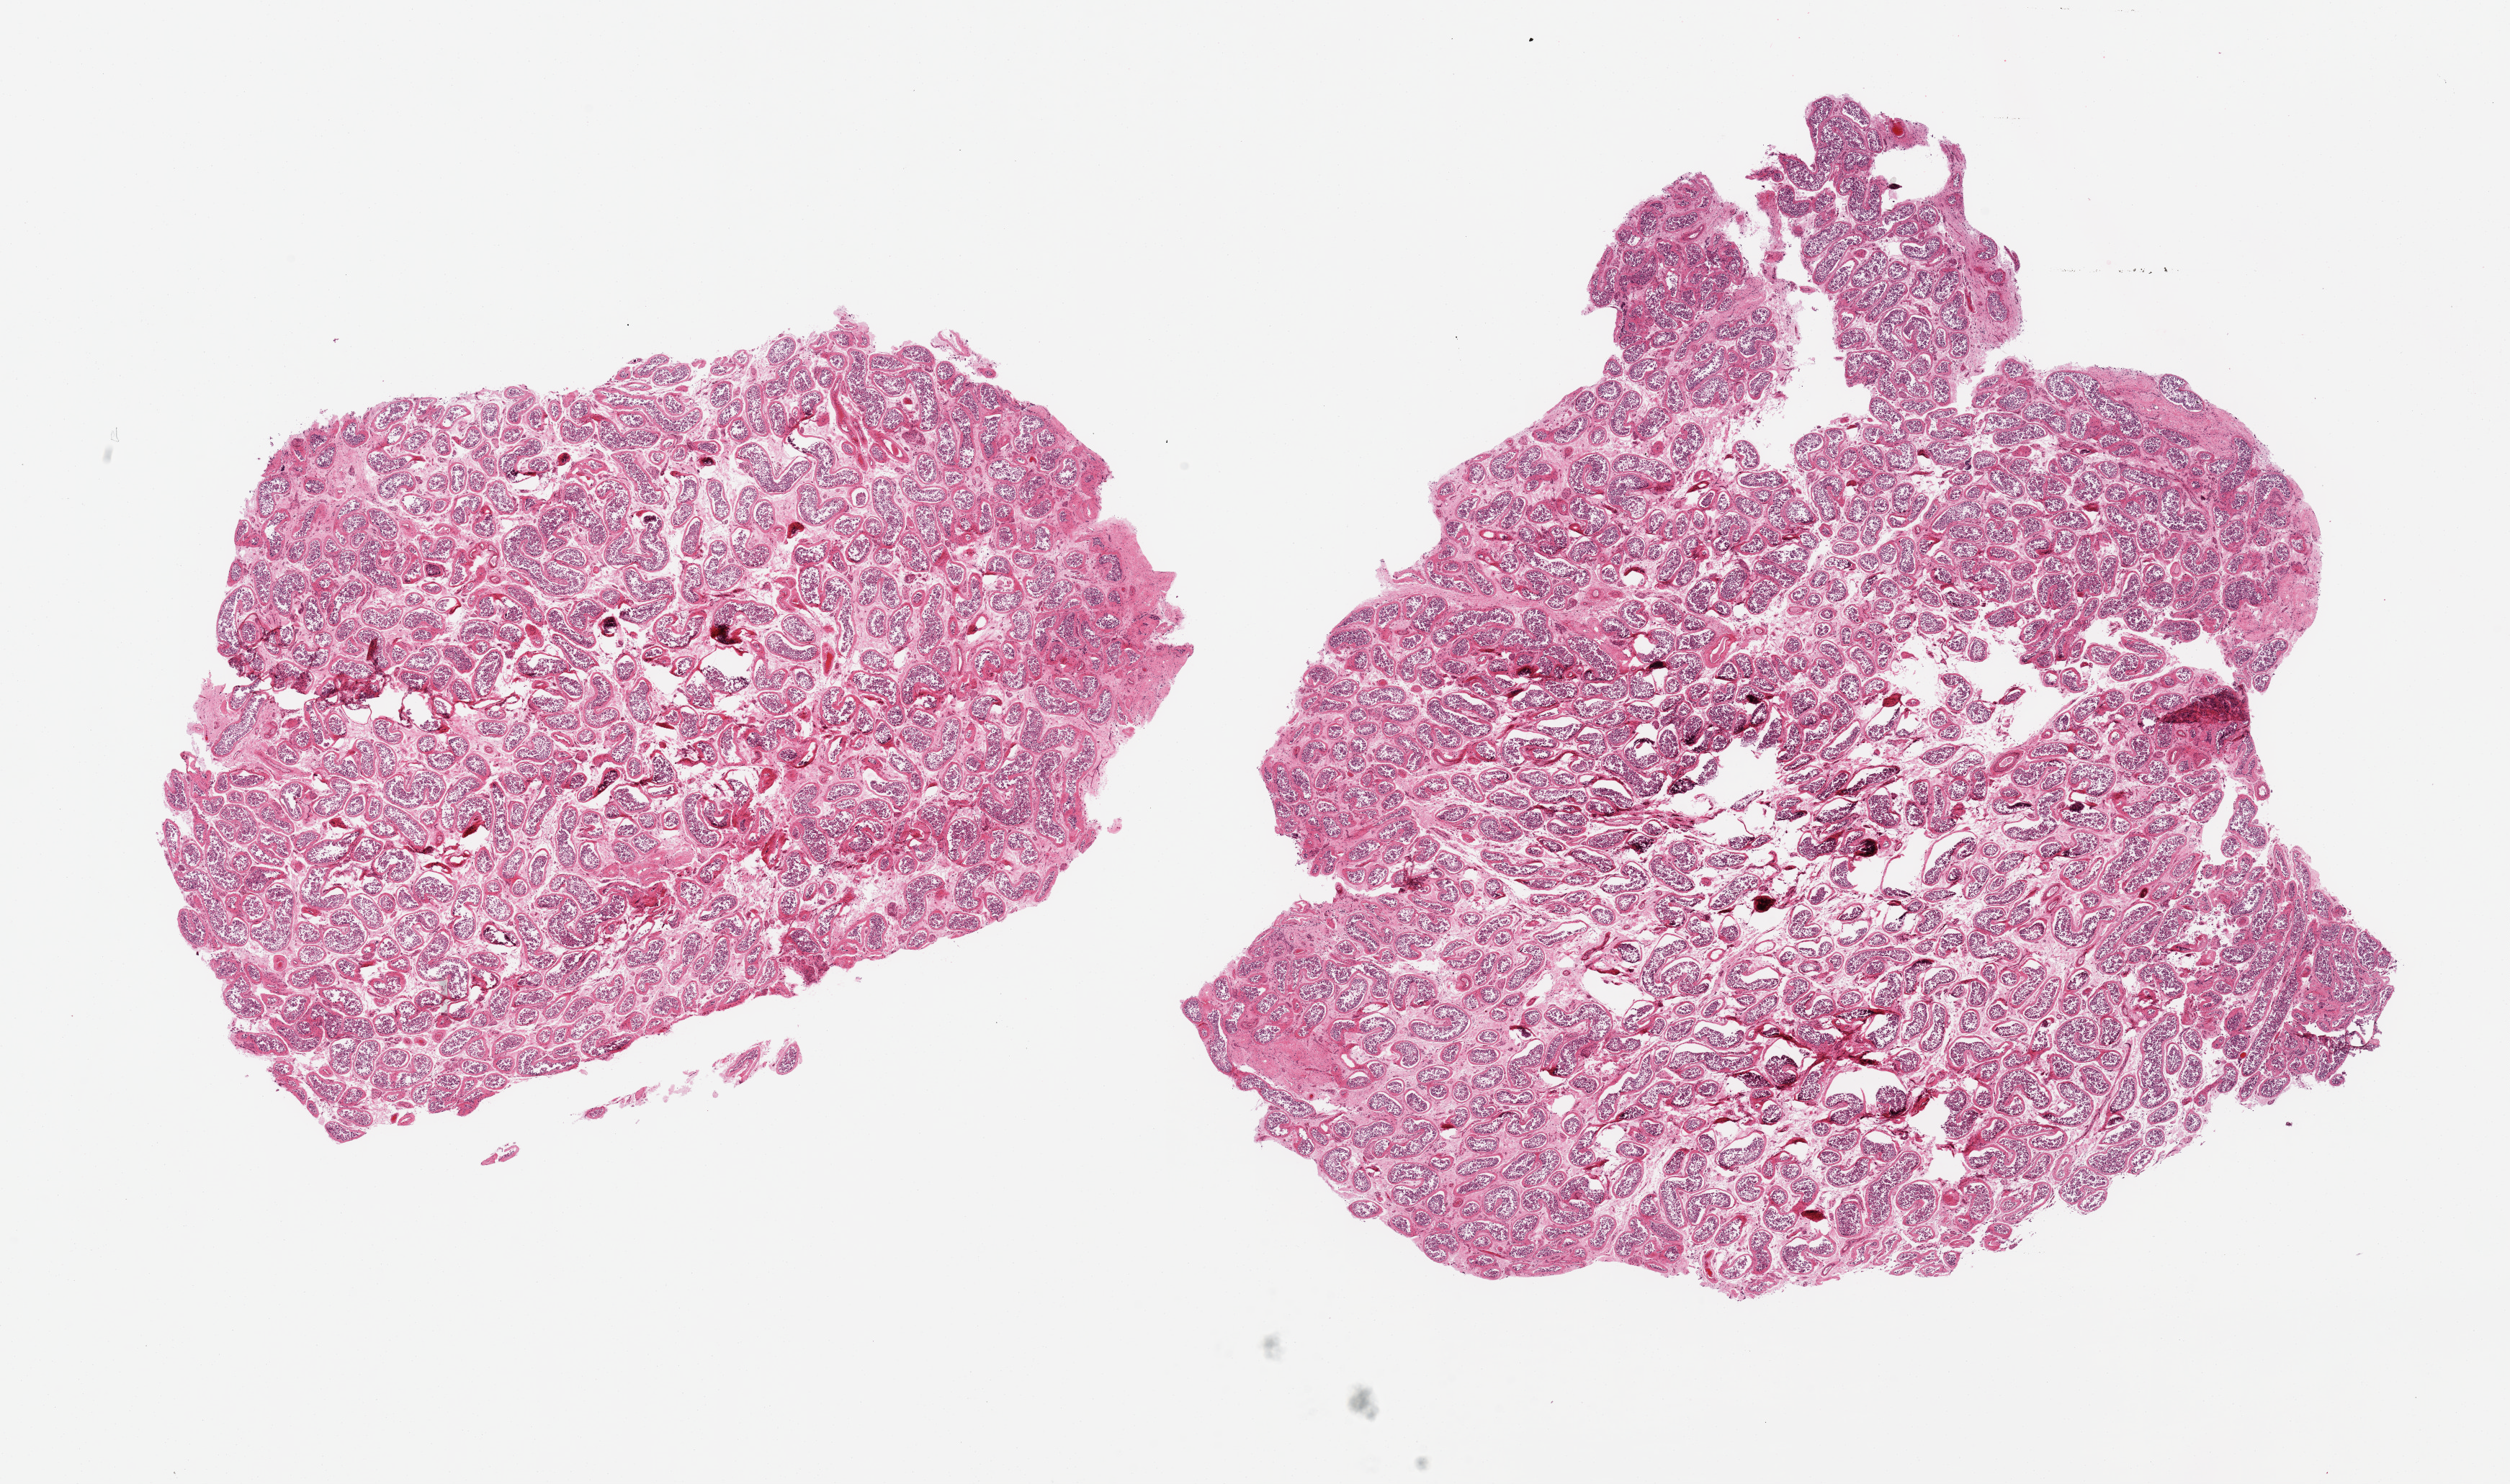
Whole-slide image, haematoxylin and eosin stain, brightfield — a low-resolution overview of the entire scanned area, about 27.6 x 16.3 mm. PAXgene-fixed, paraffin-embedded tissue. Section of testis (target tissue). Donor tissue sample. Male donor.
Review note (as recorded): 2 pieces; spermatogenesis.